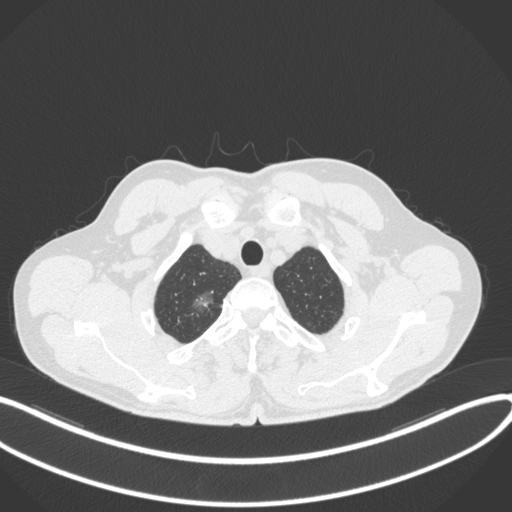
Chest CT, one axial slice; position 343 of 407 along the scan axis; lung window (W 1500 / L -600 HU); 1 mm slice thickness; 512 × 512 image matrix, field of view 400 × 400 mm. Male patient, age 58 years. From the clinical record (not read from this slice): clinical TNM (as recorded): T1c N0 M0.
Structures marked on this image (rectangle marked by the reading radiologist):
- lung tumour (recorded histology: adenocarcinoma): box from (x=189, y=286) to (x=219, y=313) px